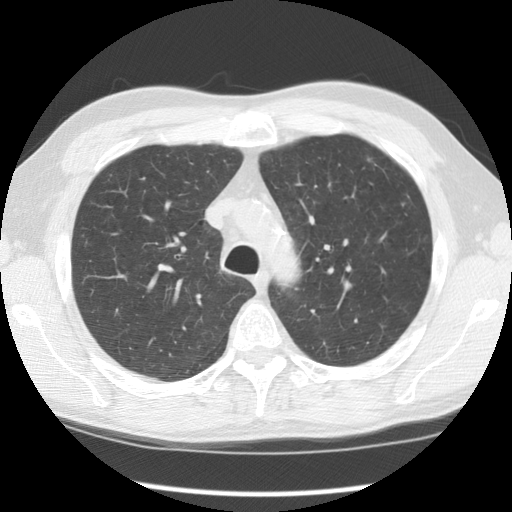
Low-dose screening chest CT, one axial slice; position 91 of 121 along the scan axis; lung window (W 1500 / L -600 HU); 2.5 mm slice thickness; 512 × 512 image matrix.
Outlined on this slice (manually delineated by an expert):
- lesion 1 (tumor, upper lobe of left lung): box from (x=368, y=159) to (x=370, y=161) px